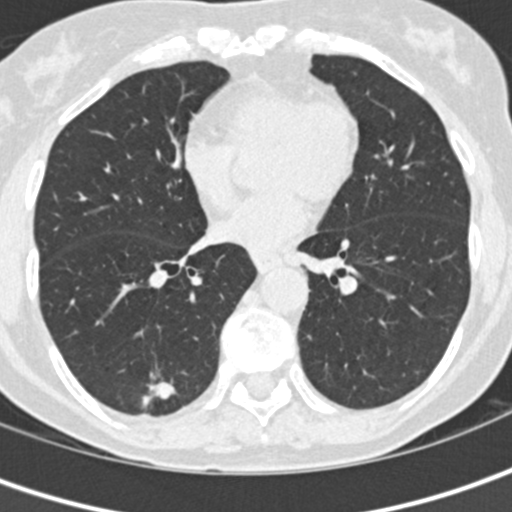
Low-dose screening chest CT, one axial slice. Slice 65 of 152 in the series (ordered by position). Lung window (W 1500 / L -600 HU). 512 × 512 image matrix.
Annotated regions visible in this slice (manually delineated by an expert):
- lesion 1 (tumor, lower lobe of right lung): box from (x=142, y=380) to (x=176, y=408) px